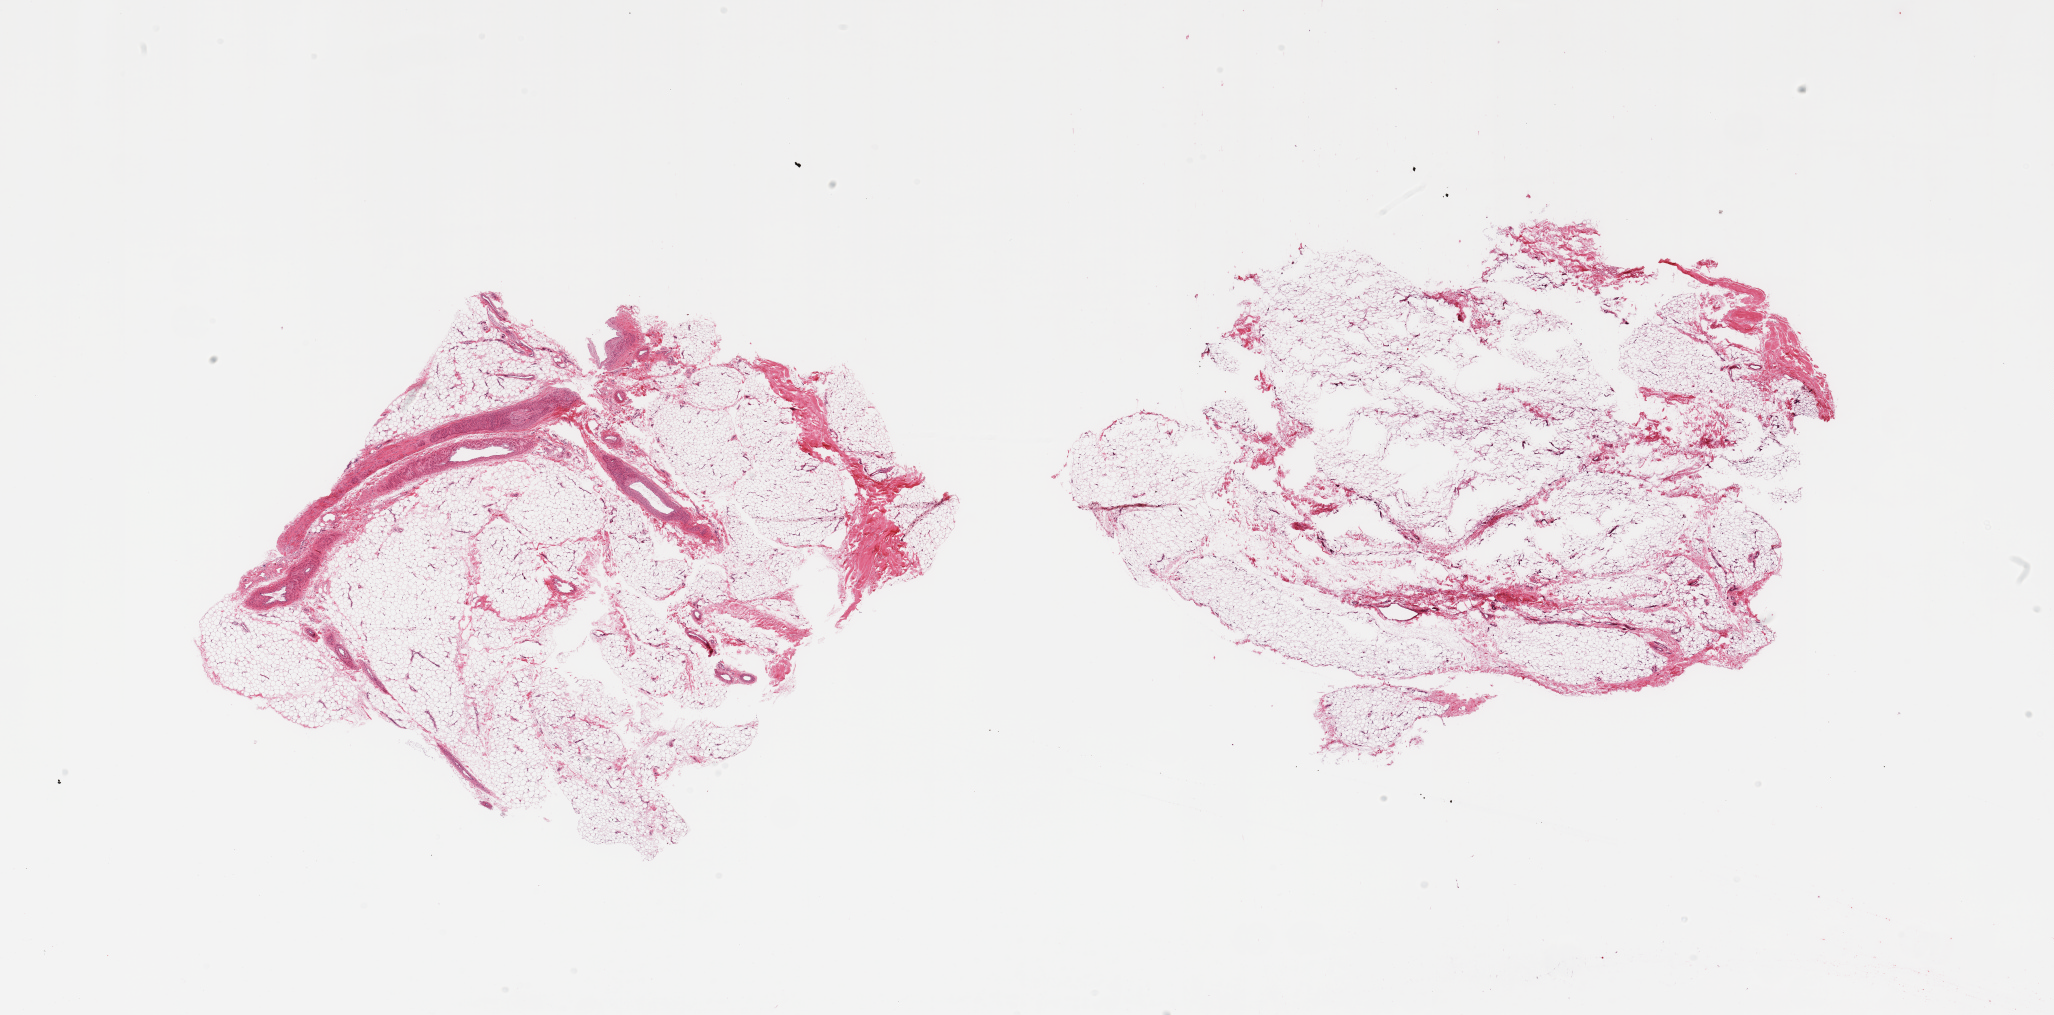
Haematoxylin and eosin whole-slide image, brightfield — whole scanned area (about 32.5 x 16.1 mm, acquisition: 20x scan) shown as a low-resolution overview; PAXgene-fixed paraffin-embedded (PFPE) section; sampled site (target tissue): adipose tissue; tissue donor sample. Male donor.
• pathologist's review note for this sample: 2 pieces; fibrovascular structures comprise 5% & 10%; internal 'holes'